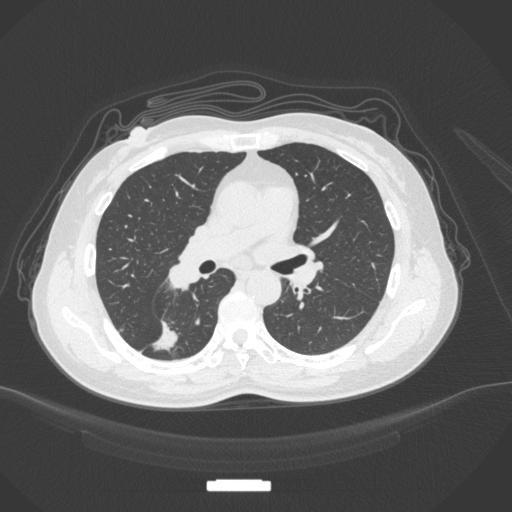
Chest CT, one axial slice. Position 172 of 352 along the scan axis. Reconstruction kernel B31f. 120 kVp. Lung window (W 1500 / L -600 HU). 1 mm slice thickness. 512 × 512 image matrix. Patient: female, 55 years. From the clinical record (not read from this slice): clinical TNM (as recorded): T1c N1 M0.
Annotated regions visible in this slice (rectangle marked by the reading radiologist):
- lung tumour (recorded histology: adenocarcinoma): bounding box <149,314,180,353> (left, top, right, bottom; pixels)